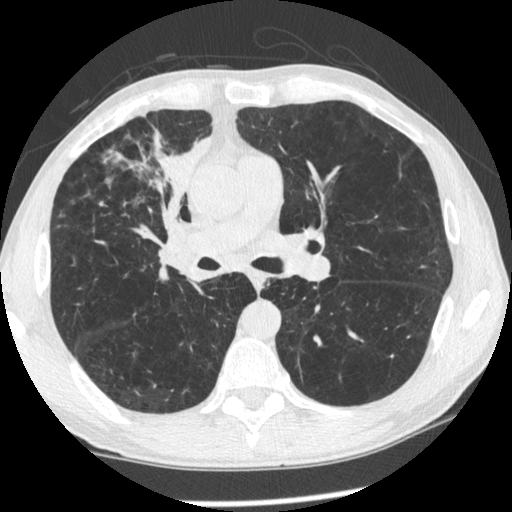
Low-dose screening chest CT, one axial slice; reconstruction kernel STANDARD; 120 kVp; lung window (W 1500 / L -600 HU); 512 × 512 image matrix, field of view 340 × 340 mm.
Structures marked on this image (expert manual segmentation):
- lesion 1 (tumor, upper lobe of right lung): bounding box [x1, y1, x2, y2] px = [151, 131, 212, 236]